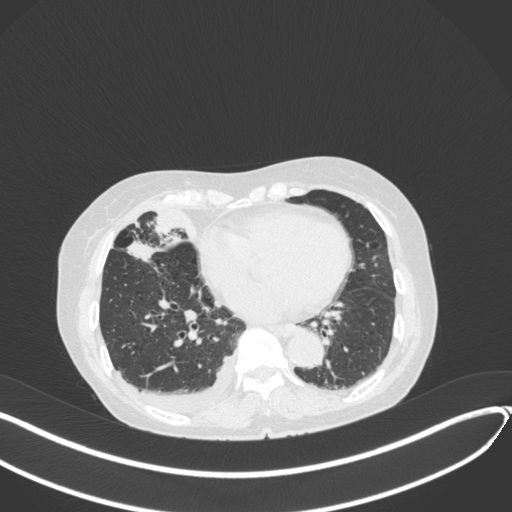
Chest CT, one axial slice; position 147 of 418 along the scan axis; reconstruction kernel B31f; 120 kVp; lung window (W 1500 / L -600 HU); 1 mm slice thickness; 512 × 512 image matrix, field of view 400 × 400 mm. Patient: female, 75 years. From the clinical record (not read from this slice): clinical TNM (as recorded): T2a N3 M0.
Outlined on this slice (rectangle marked by the reading radiologist):
- lung tumour (recorded histology: adenocarcinoma): bounding box (x1, y1, x2, y2) in pixels: (126, 238, 160, 267)